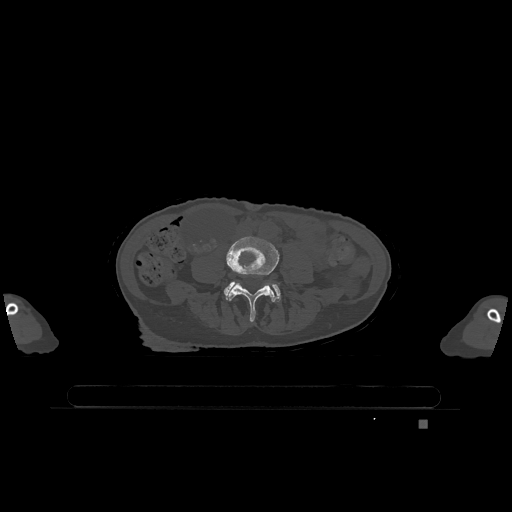
CT including the spine, one axial slice. Slice 286 of 1317 in the series (ordered by position). Bone window (W 1800 / L 400 HU). 512 × 512 image matrix, field of view 500 × 500 mm. Female patient, age 74 years. Case-level facts recorded for this patient, not image findings: primary cancer: lung.
Outlined on this slice (semi-automatically segmented with operator editing):
- L4 vertebra: bounding box [x1, y1, x2, y2] px = [226, 235, 279, 321]
- L5 vertebra: [224, 281, 281, 302]